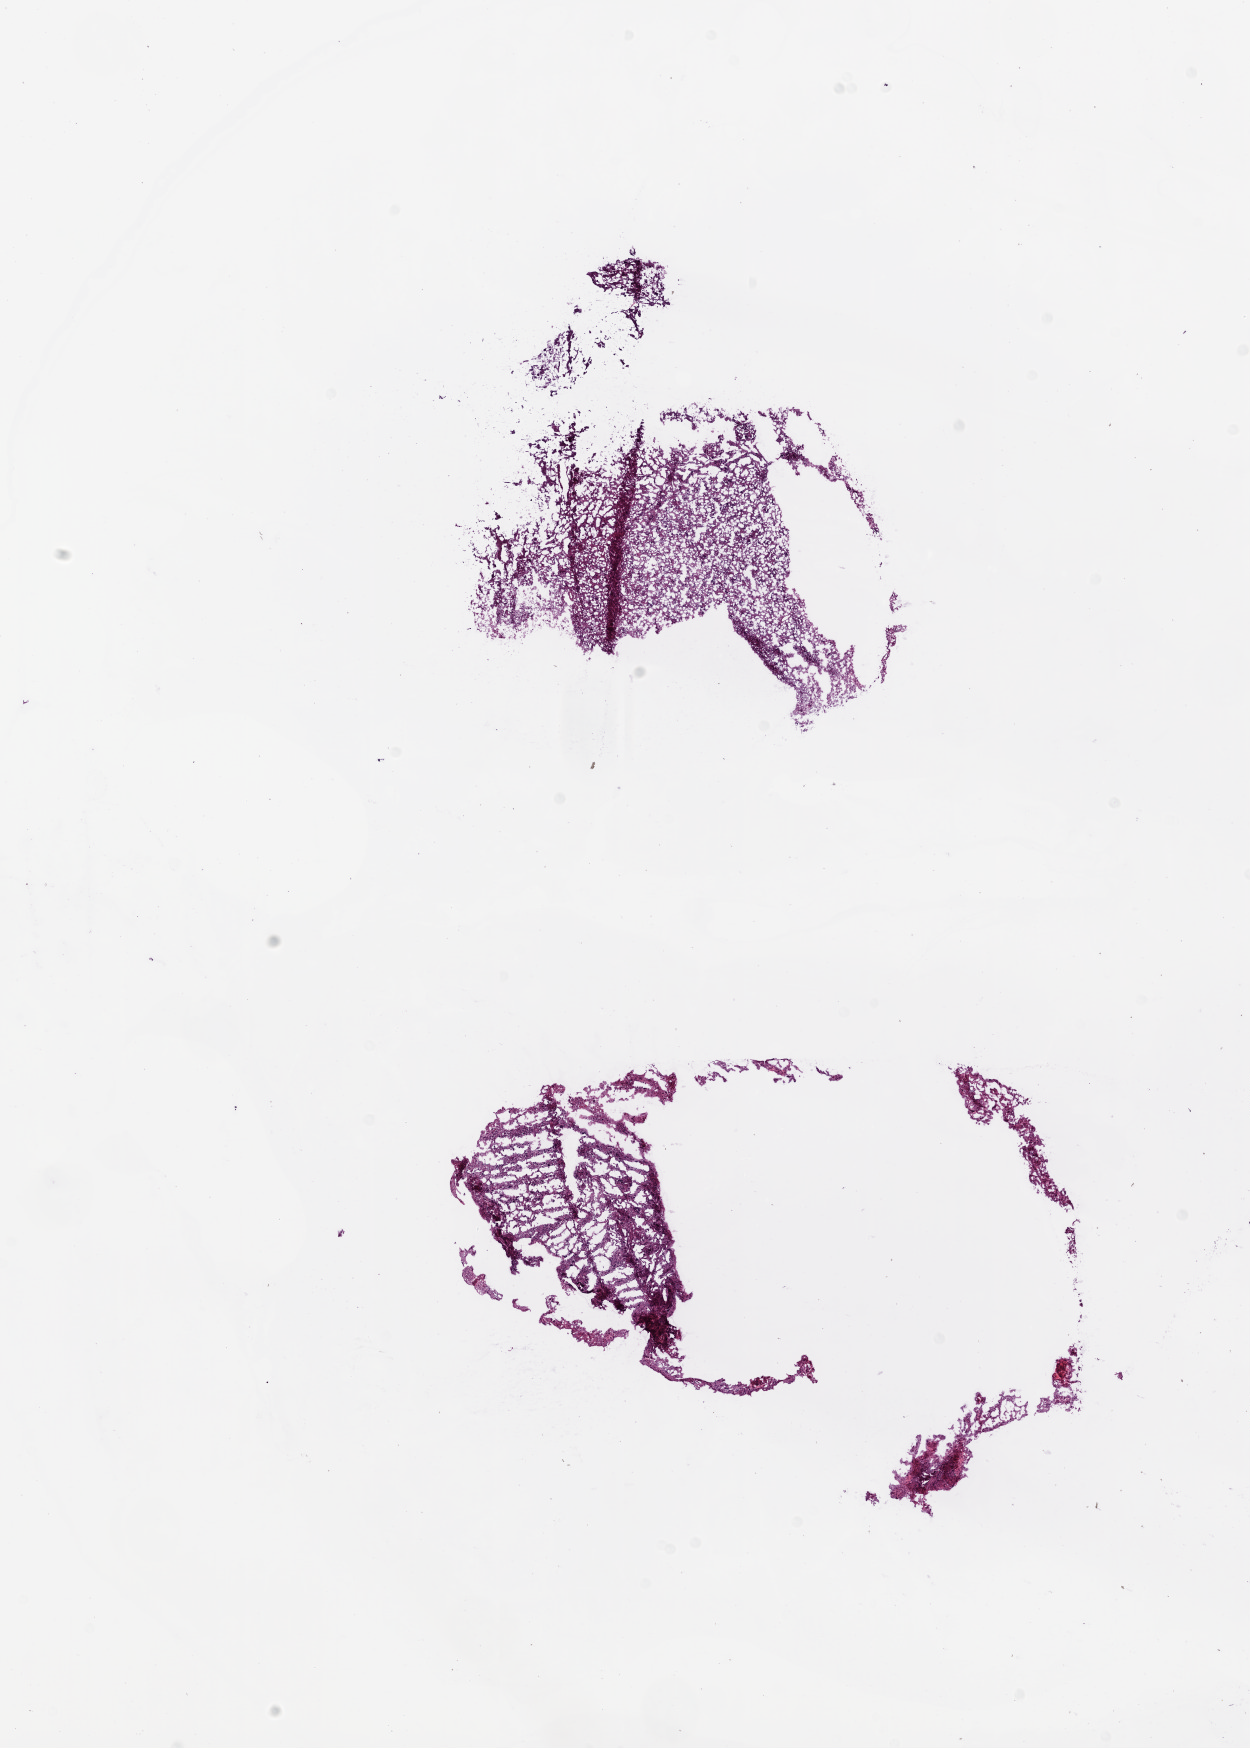
Whole-slide histology image, Hematoxylin and eosin (H&E) stained — low-resolution overview of the scanned area, about 10.0 x 14.0 mm (acquisition: 20x scan). Frozen section from the bottom of the tissue portion. Brain, primary tumour sample. Patient: female, age at initial diagnosis 53 years.
Histologic diagnosis: Glioblastoma.